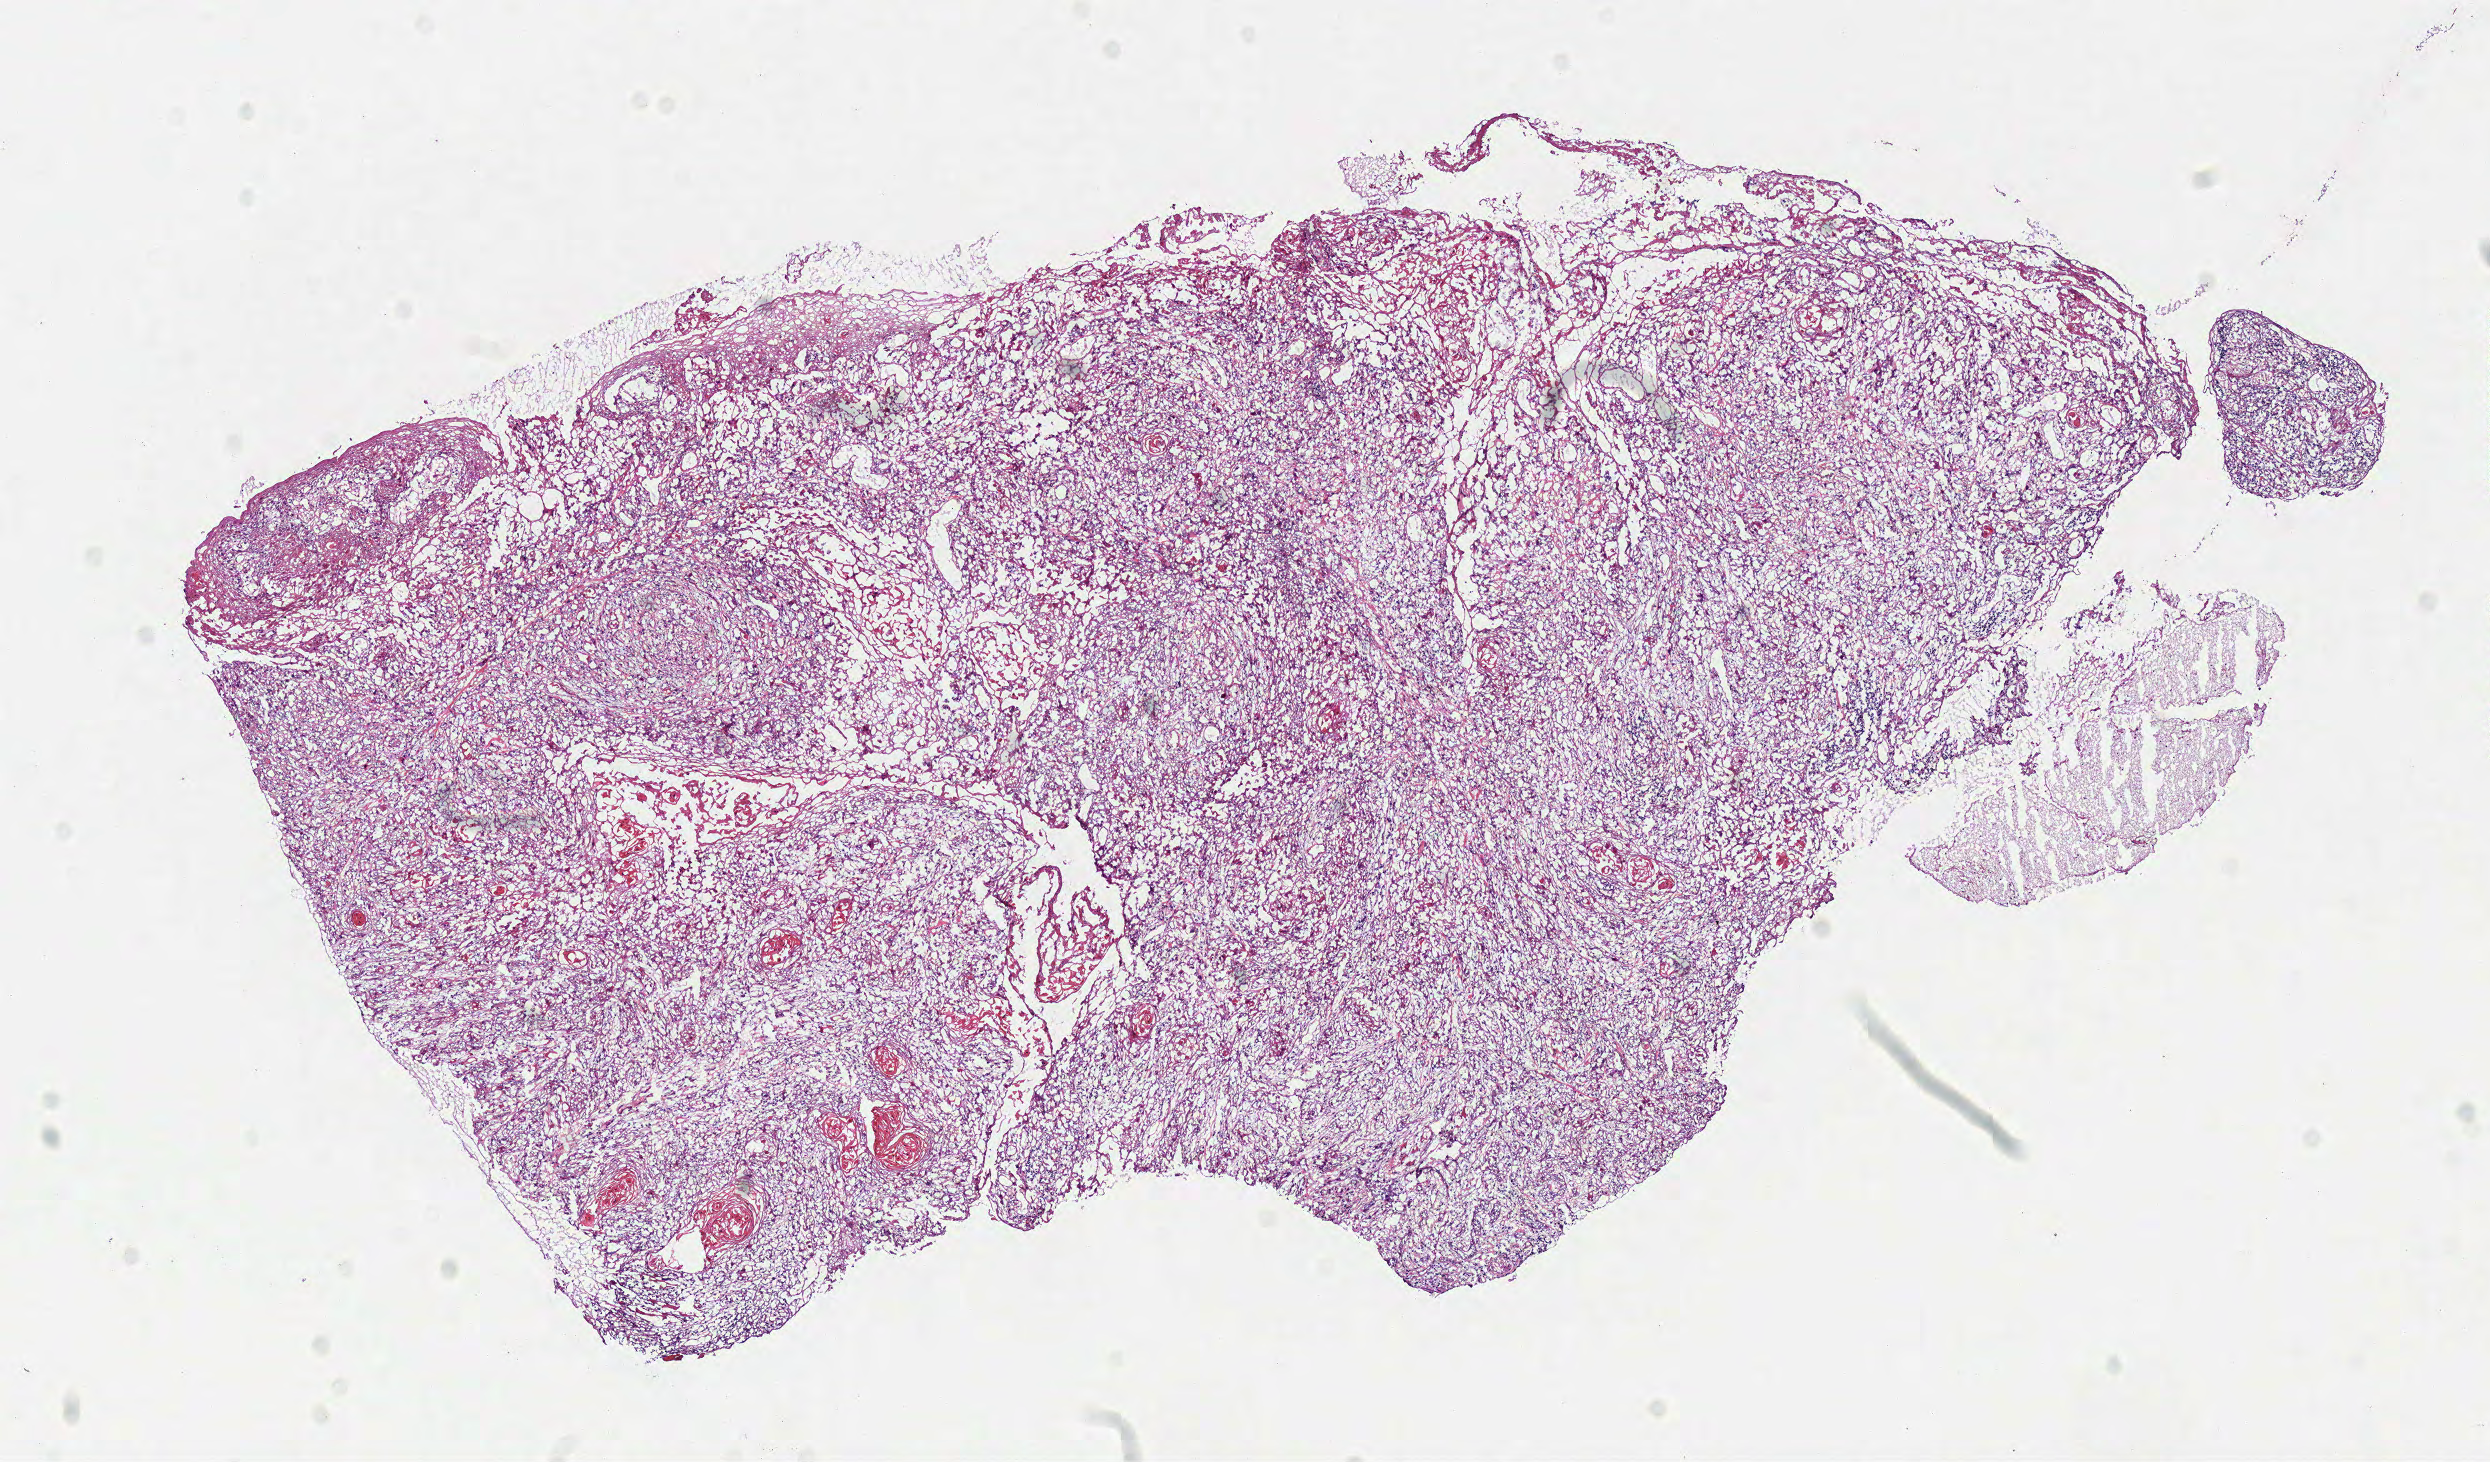
Digitized H&E-stained tissue section (whole slide) — shown as a low-resolution overview of the whole scanned area (about 9.8 x 5.7 mm, slide scanned at 40x); frozen section from the top of the tissue portion; primary tumour sample from the head and neck. Female patient; age at initial diagnosis 43 years. Slide review estimates, as recorded: tumour cells 84%, tumour nuclei 80%.
Histologic diagnosis: Squamous cell carcinoma, NOS (tongue, NOS).